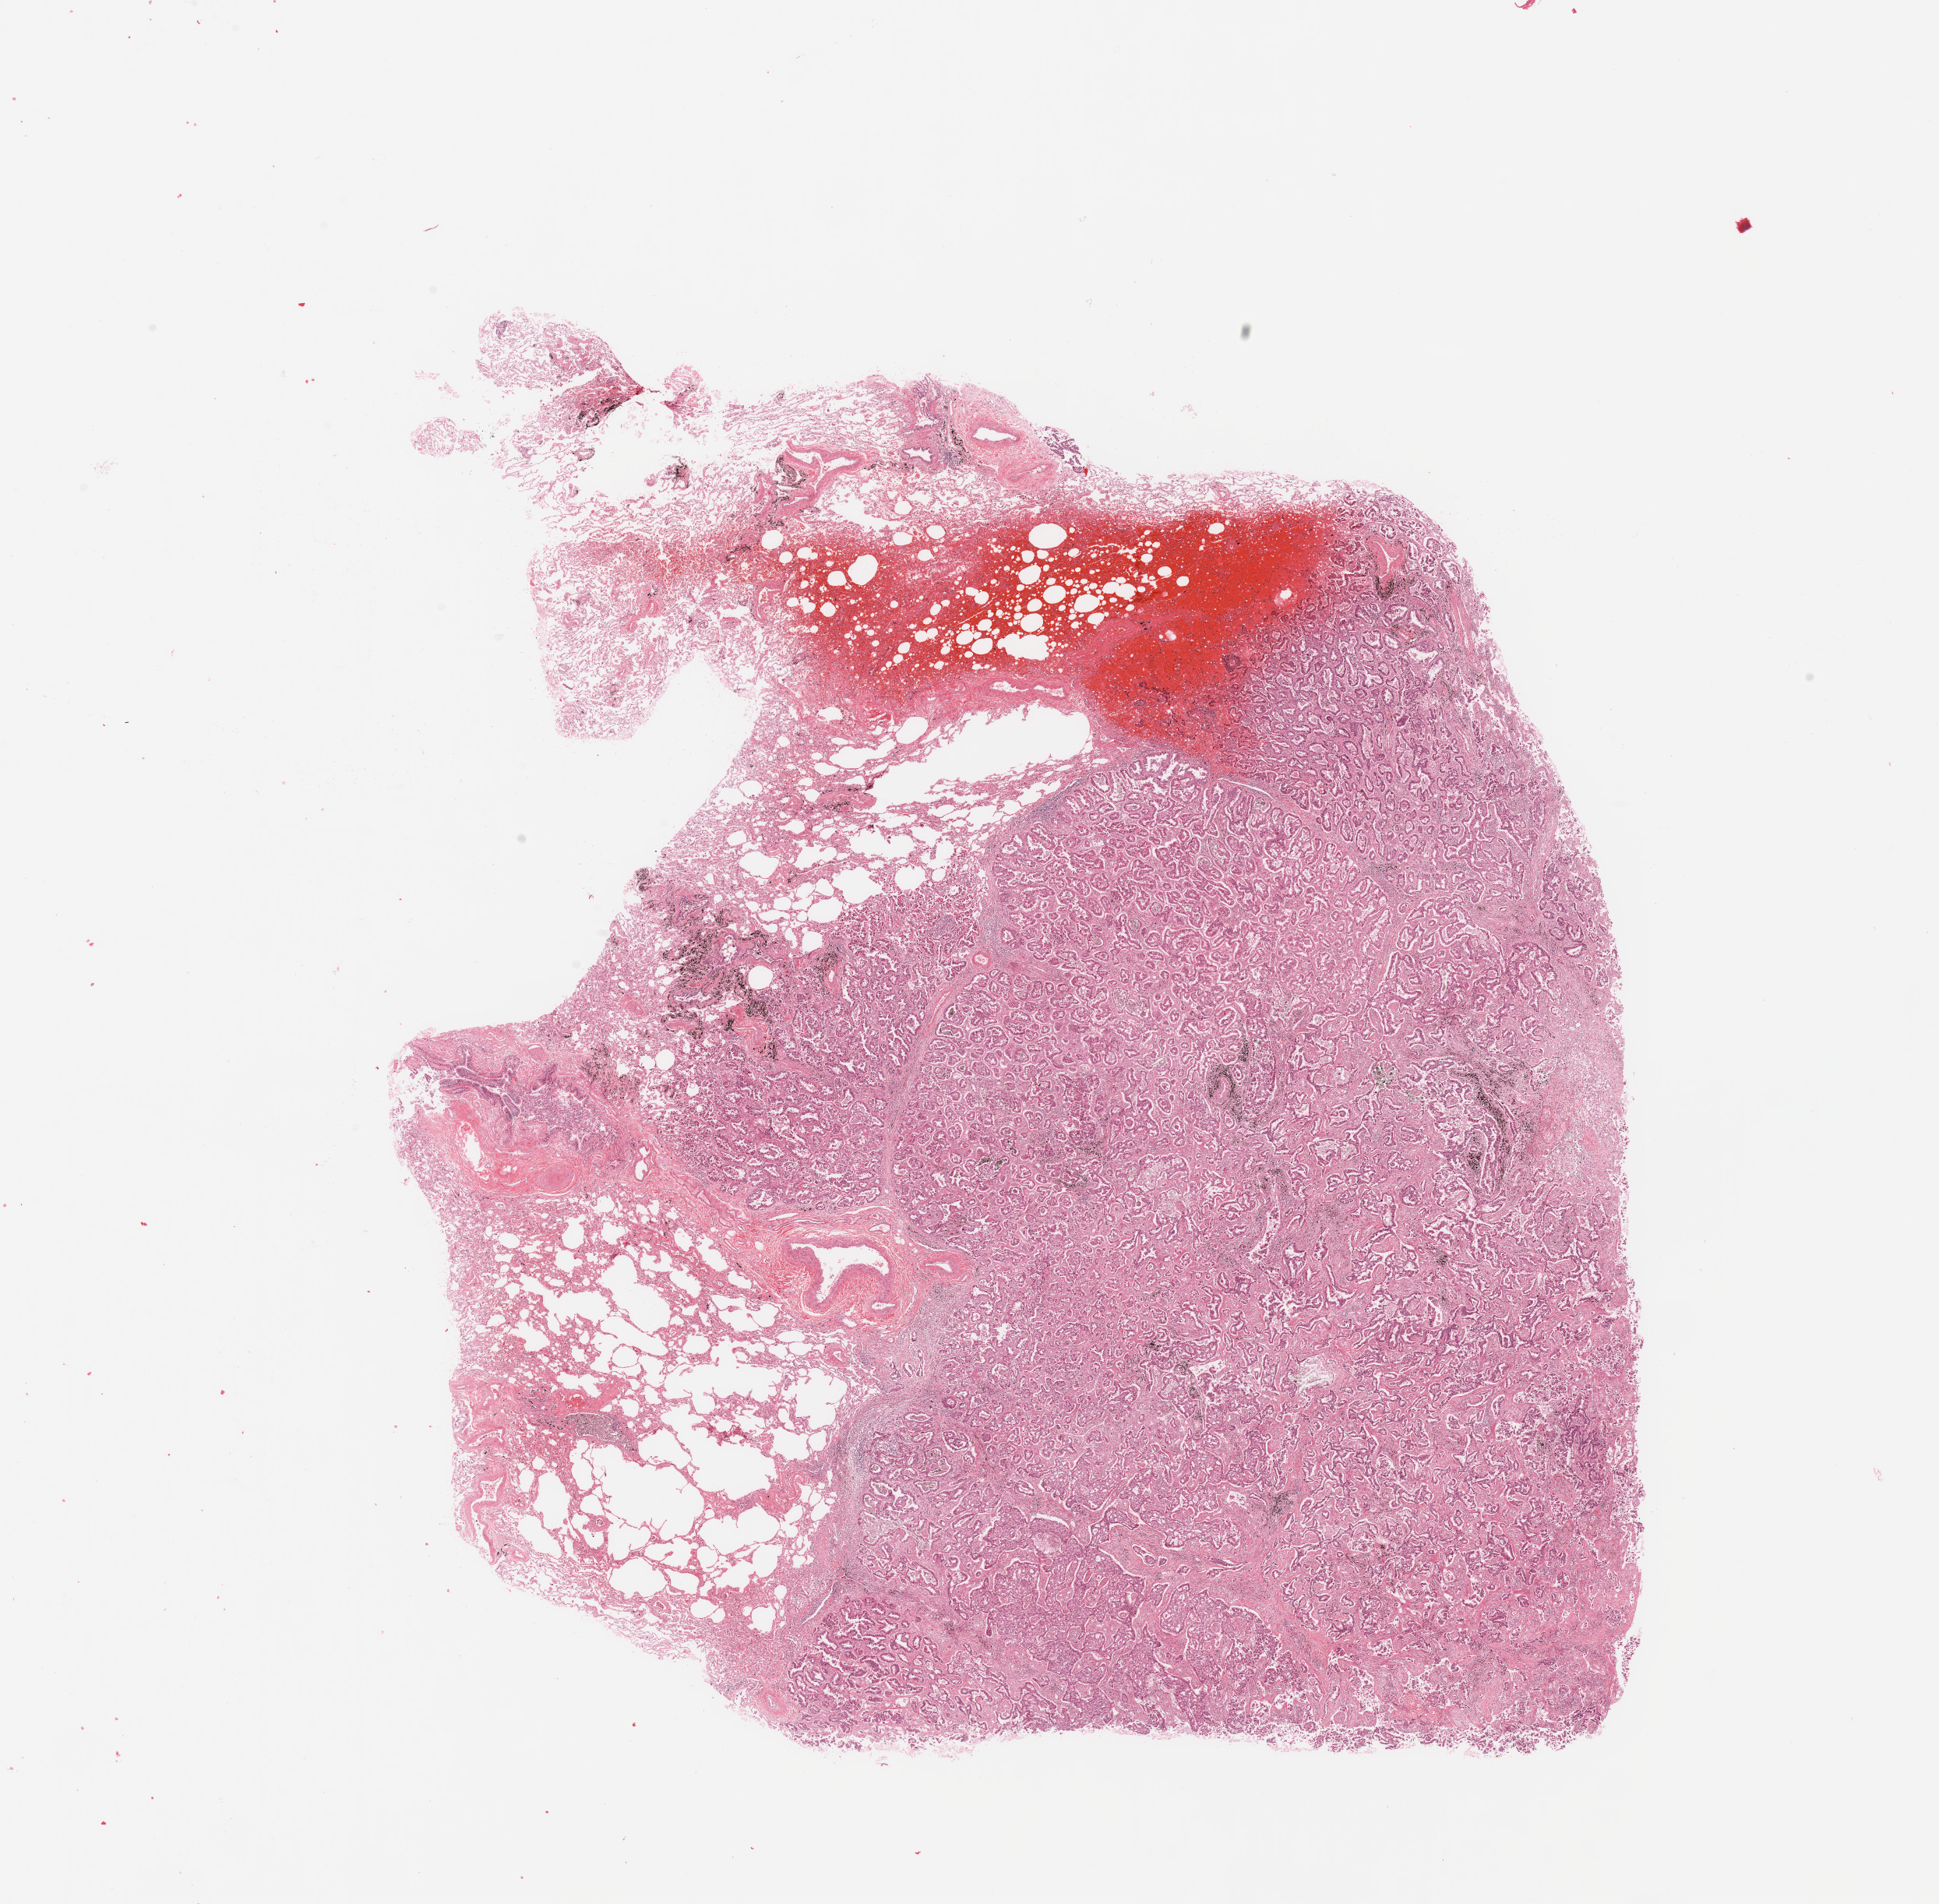
Digitized H&E-stained tissue section (whole slide), low-resolution overview of the scanned area, about 19.7 x 19.3 mm (slide scanned at 20x), lung, tumour tissue. Patient: female, age 55 years. Histologic grade: G2 (moderately differentiated).
AJCC pathologic stage: IA. Histologic diagnosis: Adenocarcinoma, NOS.